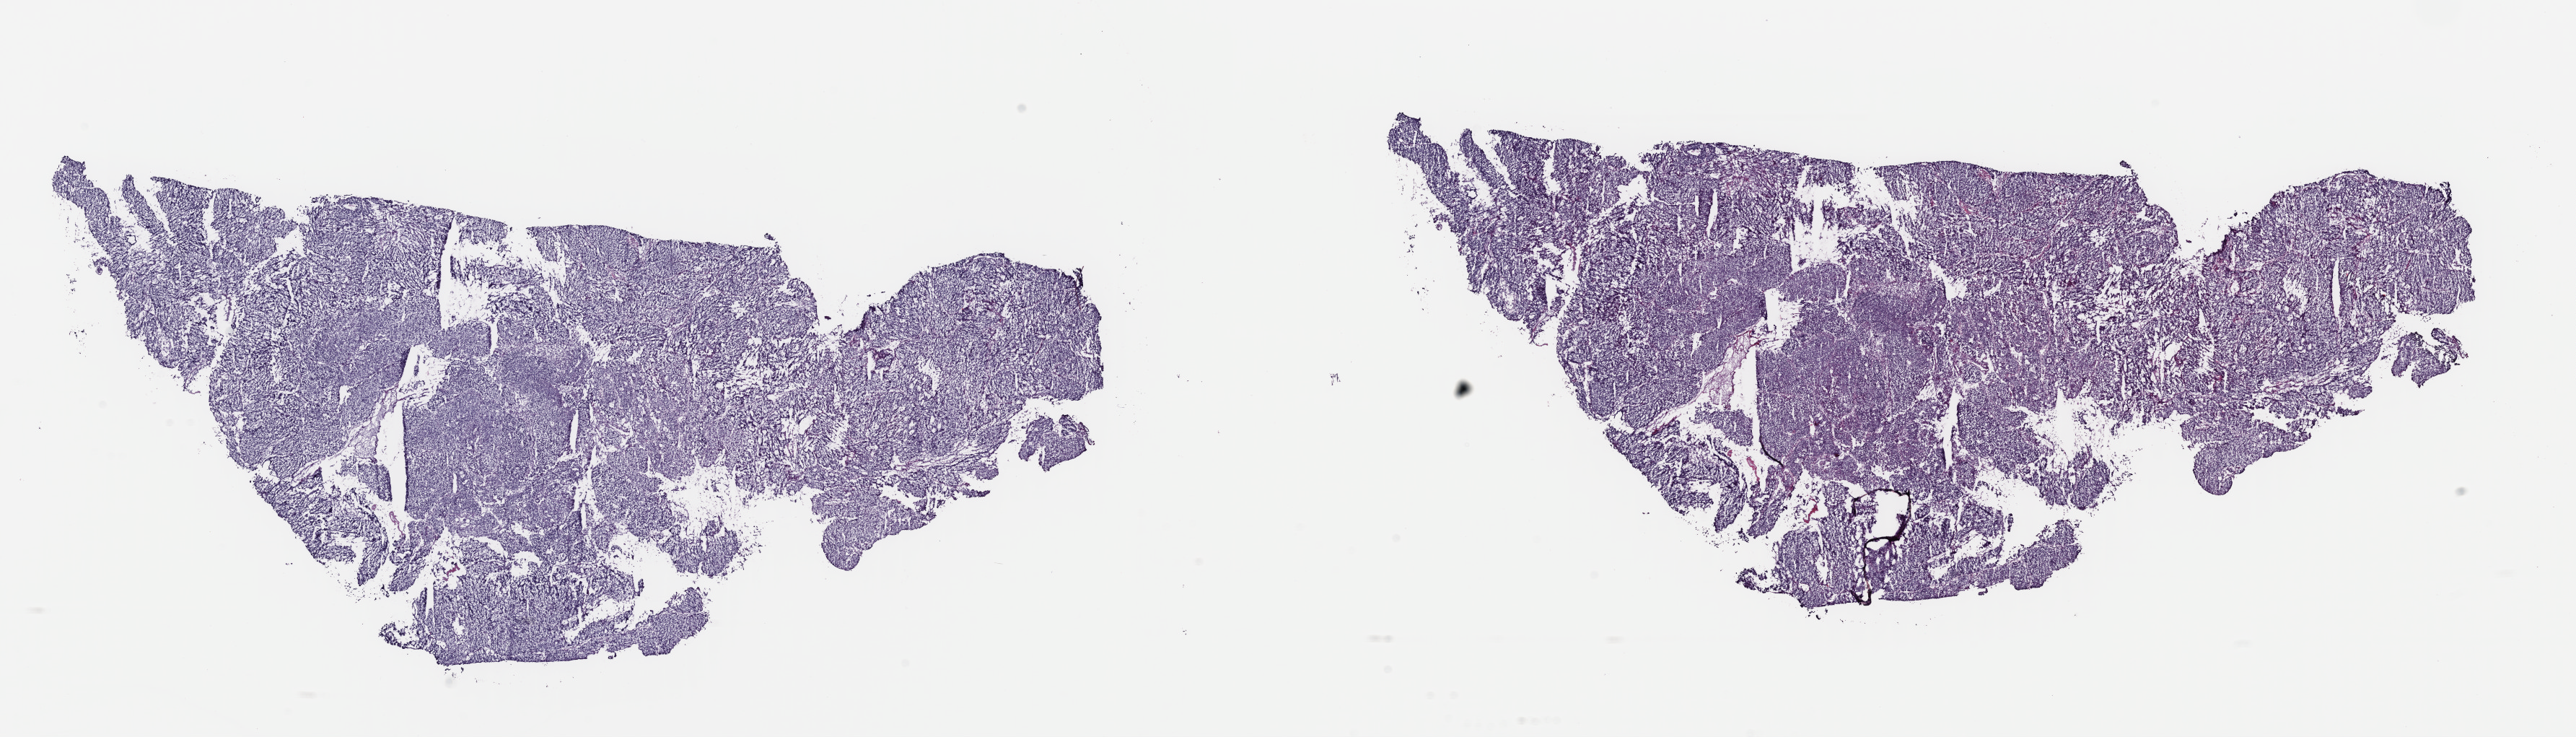
H&E whole-slide image, shown as a low-resolution overview of the whole scanned area (about 28.2 x 8.1 mm, from a 40x scan), frozen section from the top of the tissue portion, primary tumour sample from the uterus. Patient: female, age at initial diagnosis 69 years. Histologic grade: G3 (poorly differentiated). Composition of this section per pathologist review: tumour cells 90%, tumour nuclei 90%, normal cells 0%, stromal cells 5%, necrosis 5%. Infiltration values recorded for this section: lymphocyte infiltration 40%, monocyte infiltration 10%, neutrophil infiltration 30%.
• pathologic diagnosis: Endometrioid adenocarcinoma, NOS (endometrium)
• FIGO stage: IA